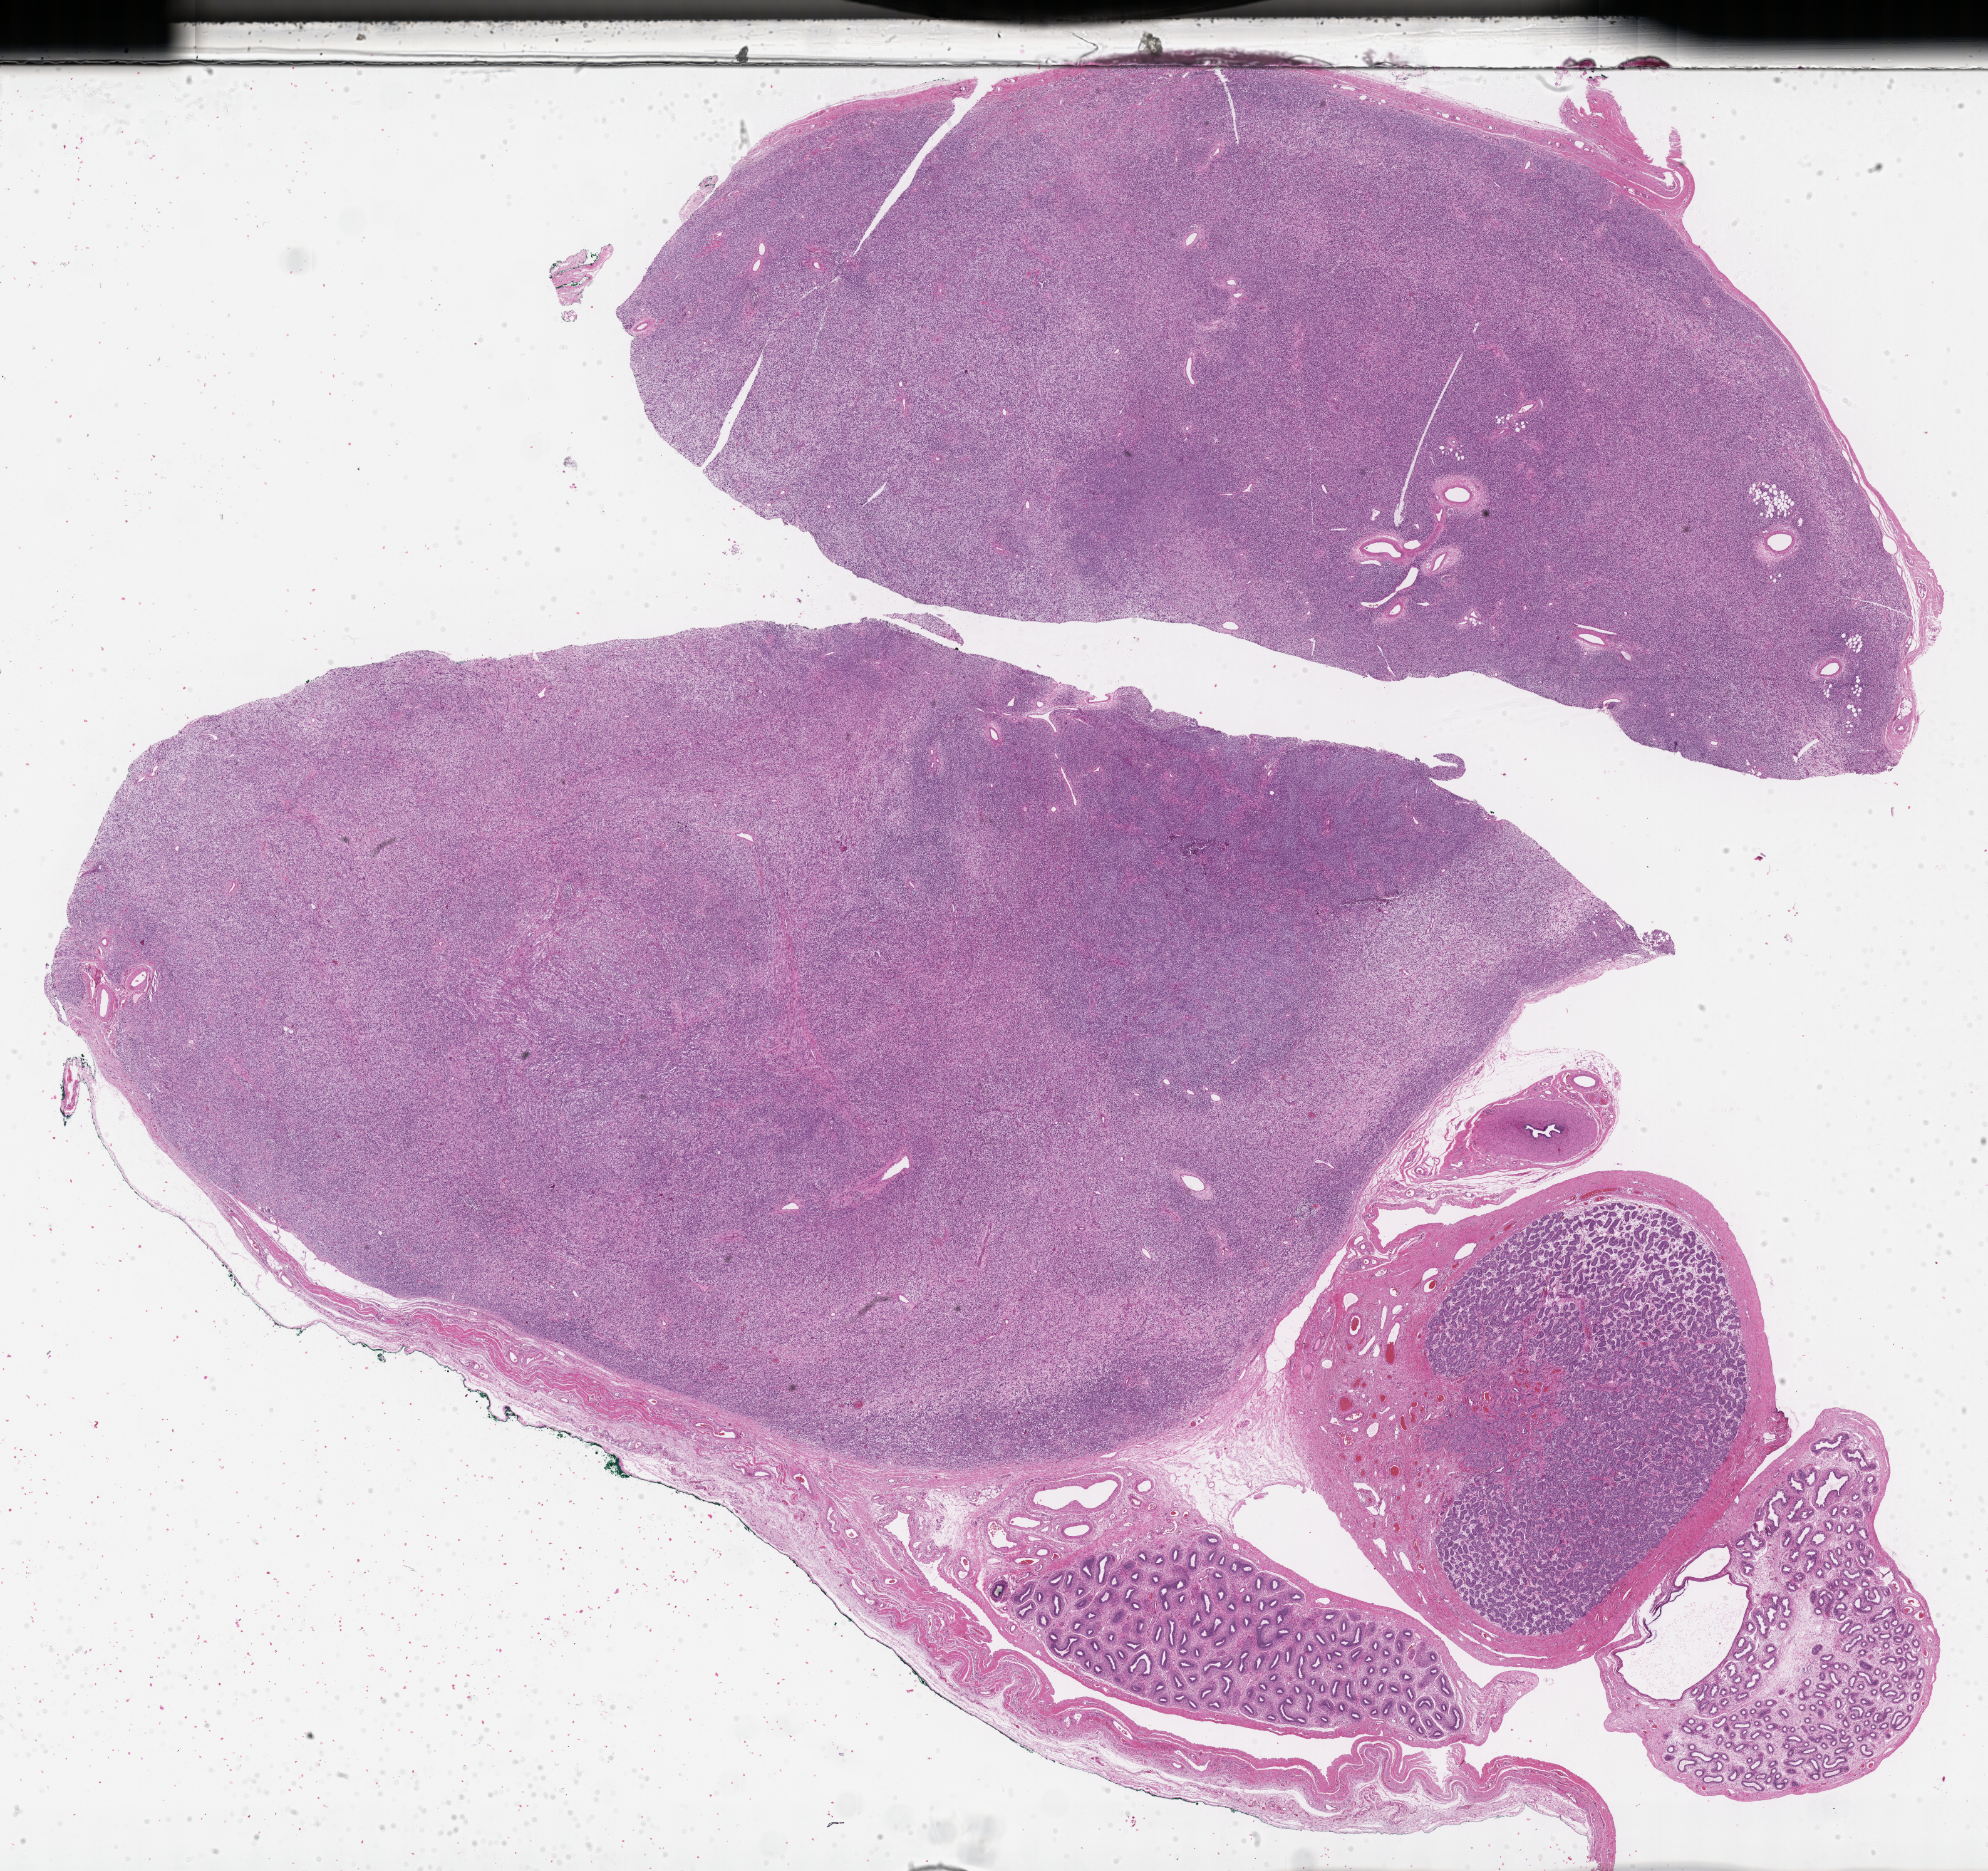
Haematoxylin and eosin whole-slide image of tumor tissue, whole scanned area (about 25.7 x 24.1 mm) shown as a low-resolution overview; FFPE section; sample anatomic site: testicle-left. Patient: male, age 1.2 years at diagnosis.
Diagnosis: rhabdomyosarcoma; histological classification: embryonal rhabdomyosarcoma. Stage (as recorded): 1. Metastatic status at presentation (as recorded): non-metastatic. Primary site (case record): testis-Paratestis.